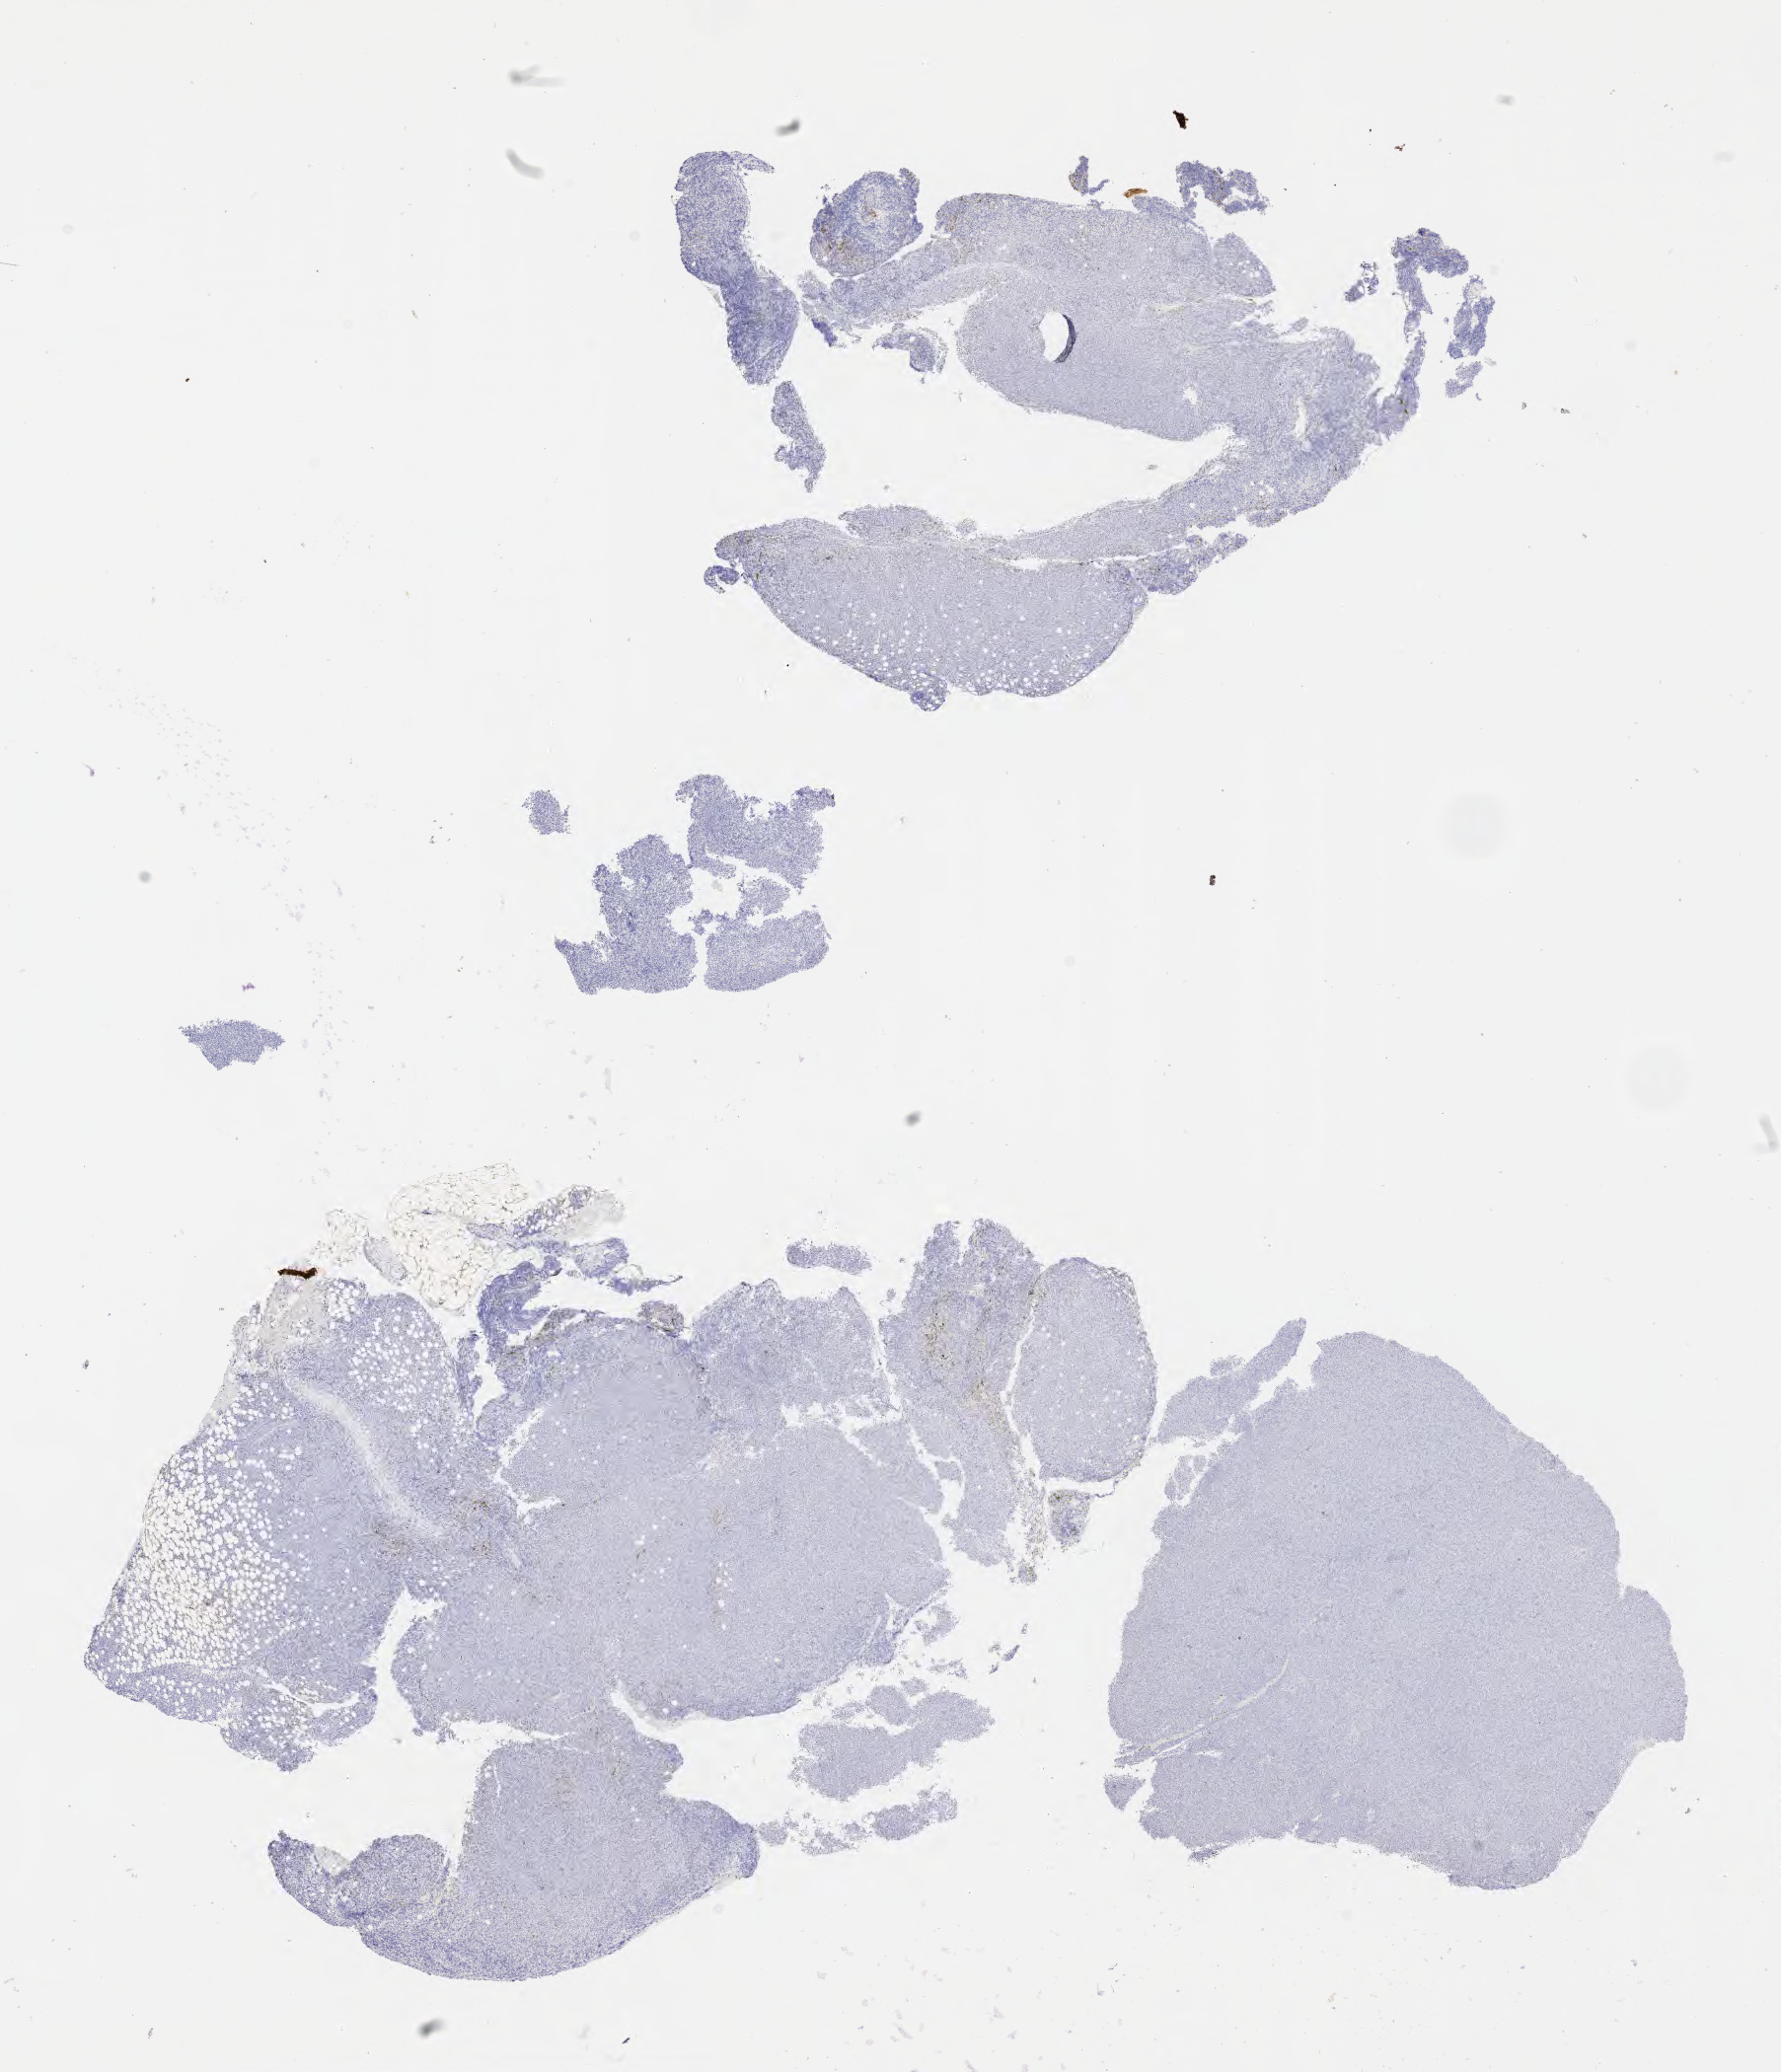
Immunohistochemistry (IHC) whole-slide image stained for CD10, a low-resolution overview of the entire scanned area, about 14.6 x 17.0 mm. Tumor tissue. Female patient, age 32 years.
Histologic diagnosis: Diffuse large B-cell lymphoma, NOS.